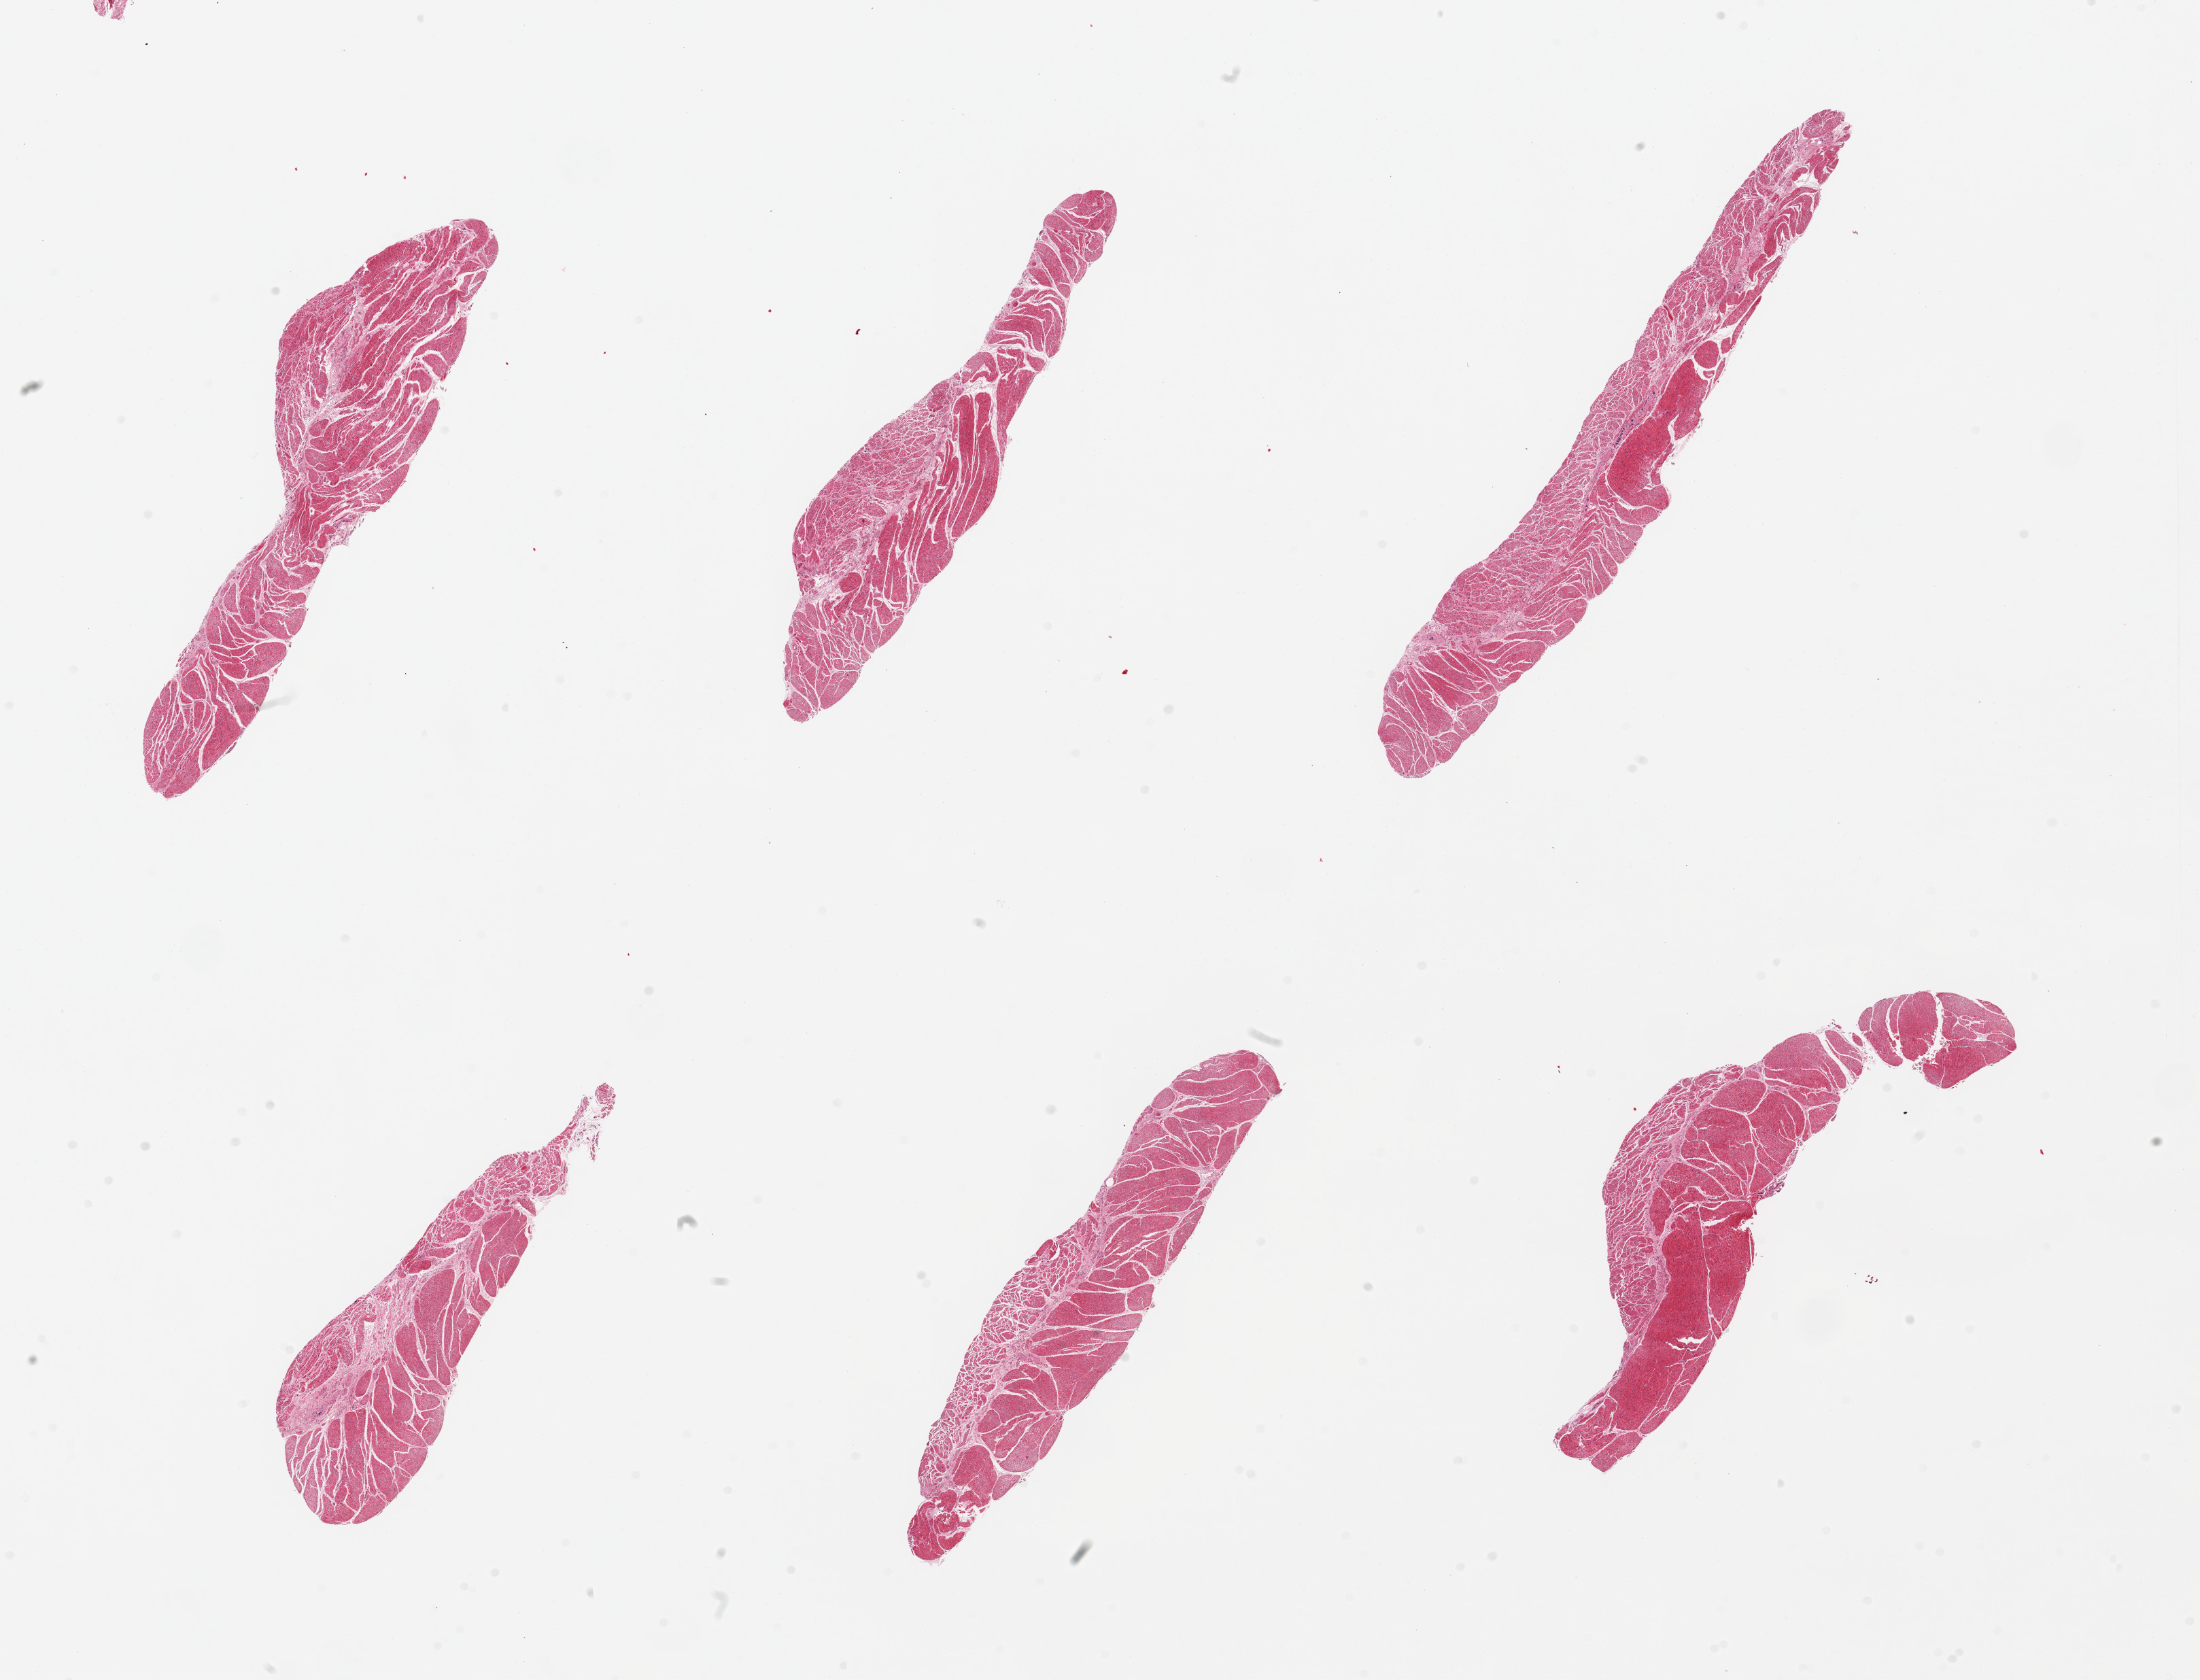
Digitized haematoxylin and eosin-stained section, low-resolution overview of the scanned area, about 25.6 x 19.5 mm (acquisition: 20x scan); PAXgene-fixed paraffin-embedded (PFPE) section; target tissue: esophageal muscle; tissue donor sample.
Review note (as recorded): 6 pieces, all targetr muscularis, good specimens.